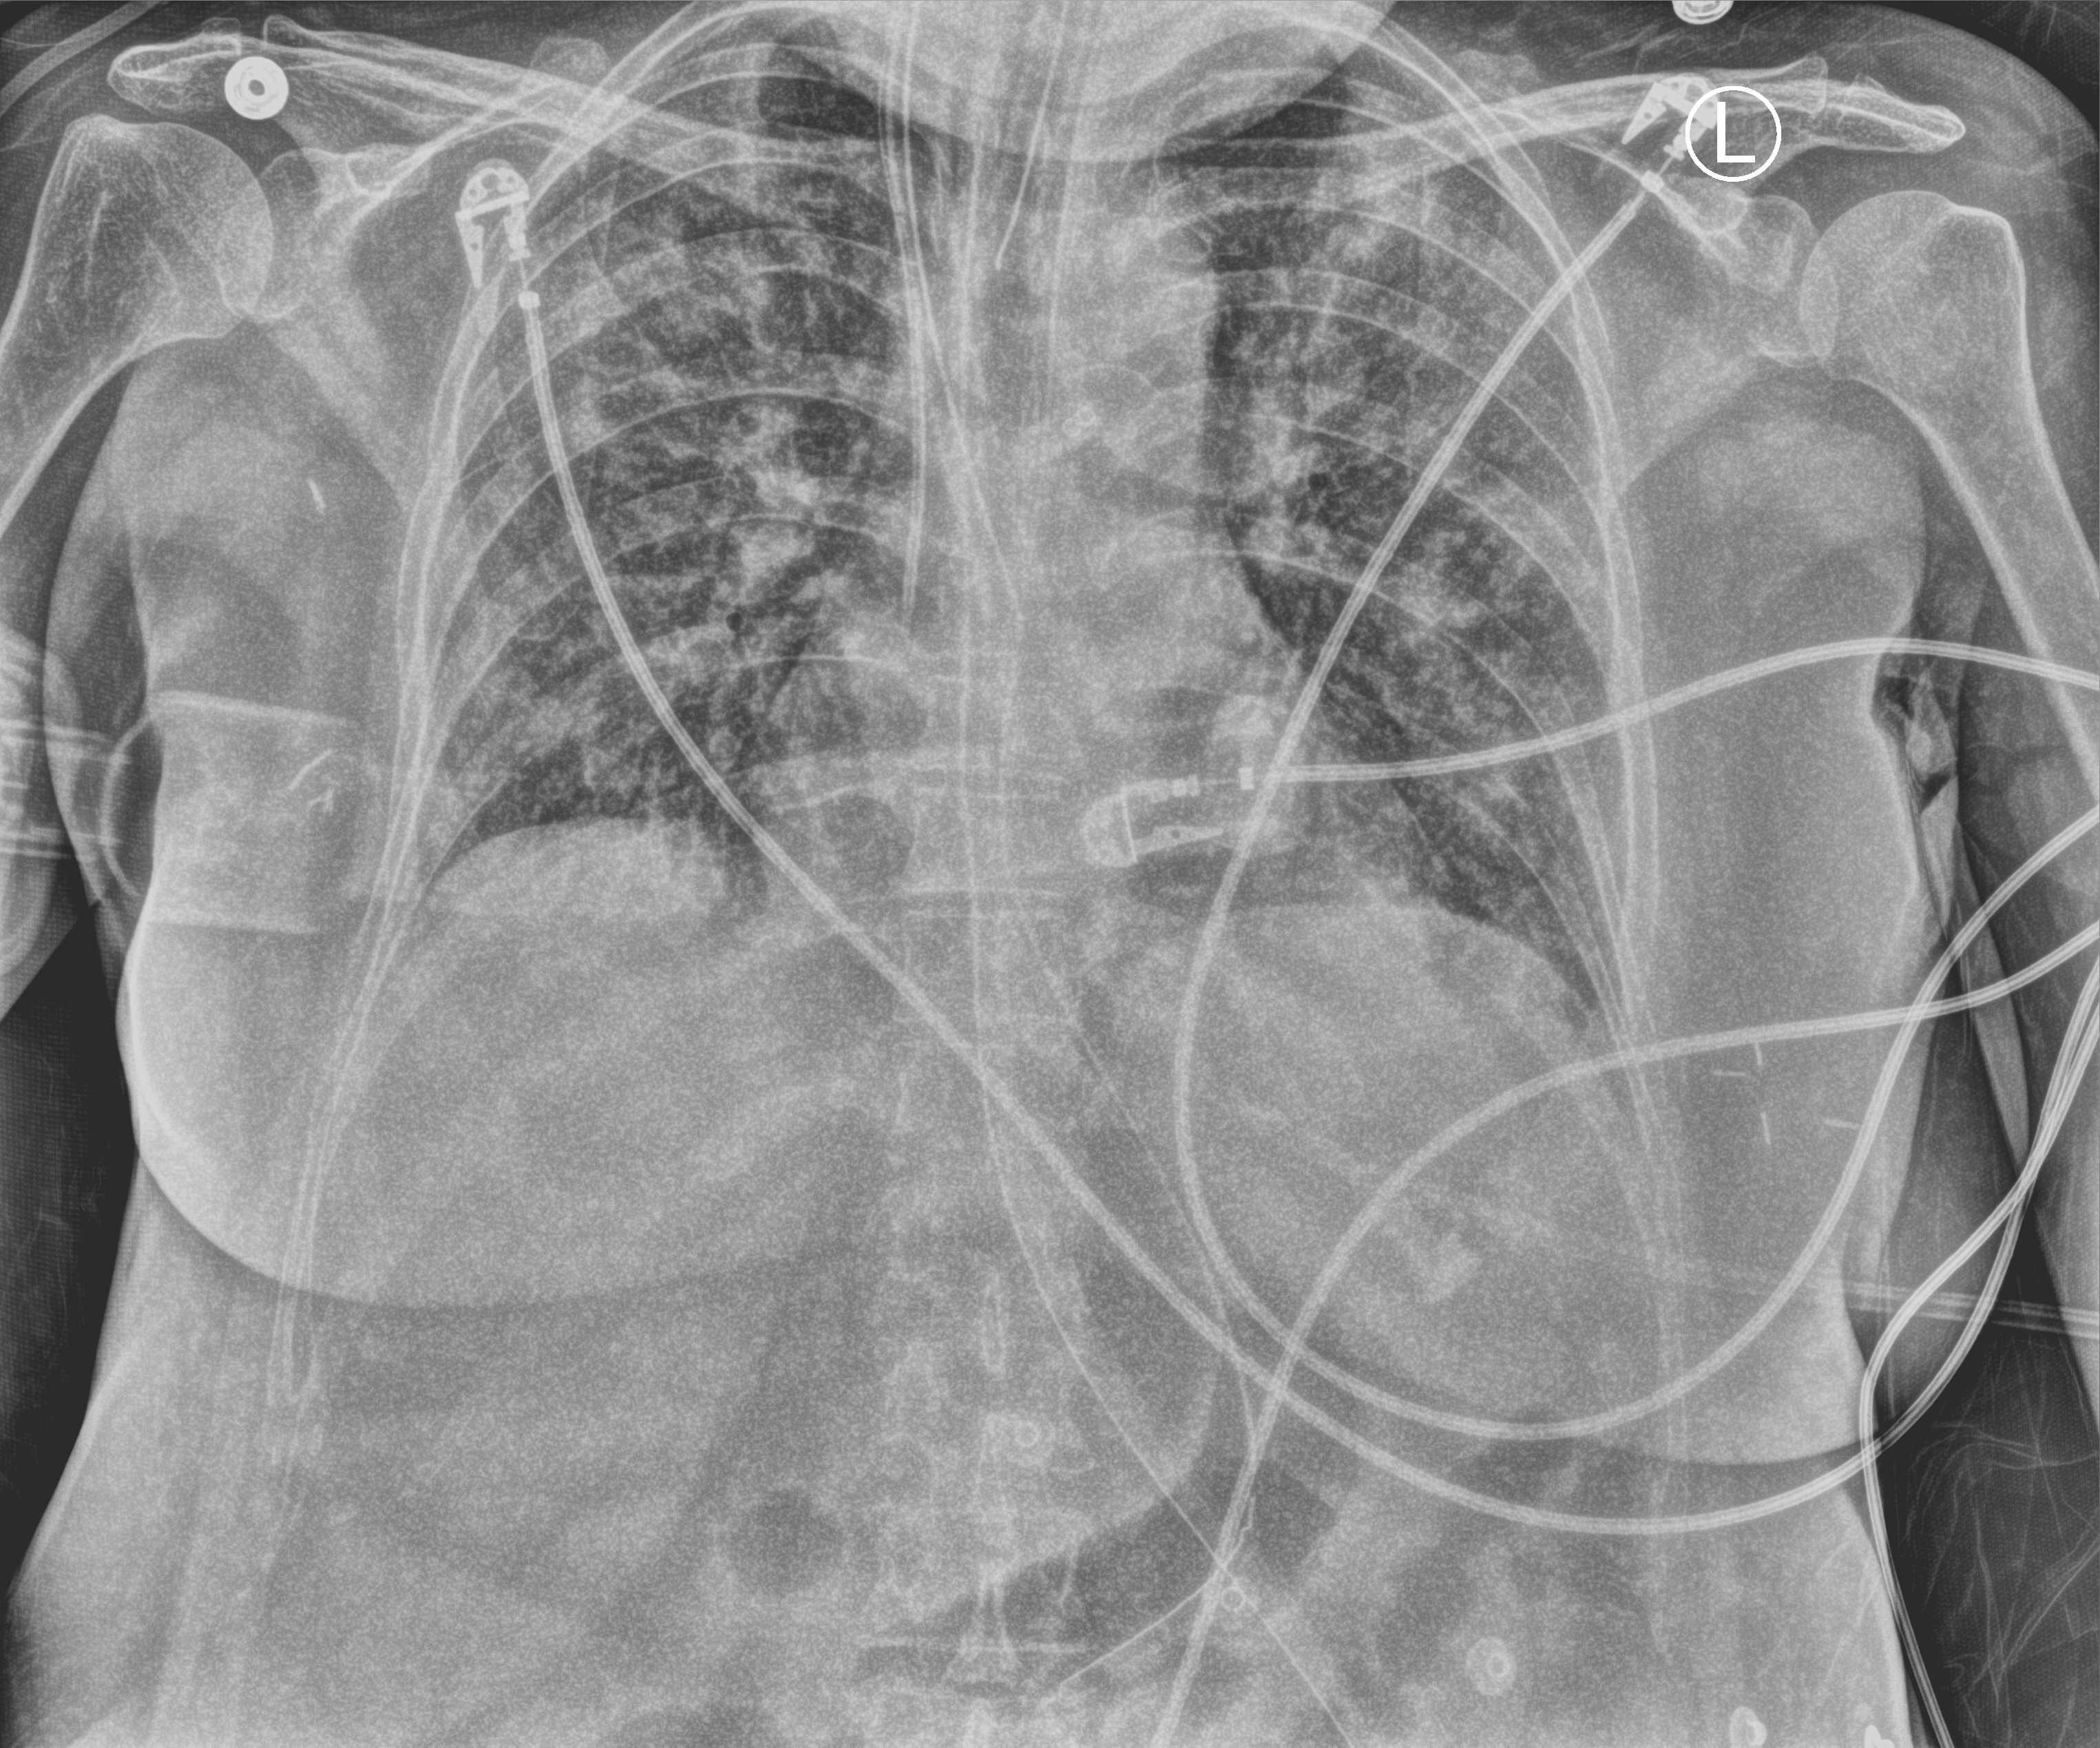
Portable chest radiograph, anteroposterior (AP) projection. Female patient hospitalised with COVID-19, age 18–59 years.
Hospital-stay facts (about this admission, not read from this image; timing relative to this image not recorded):
- diabetes (admission record): no
- mechanically ventilated during this hospital stay: yes
- admitted to intensive care during this hospital stay: no